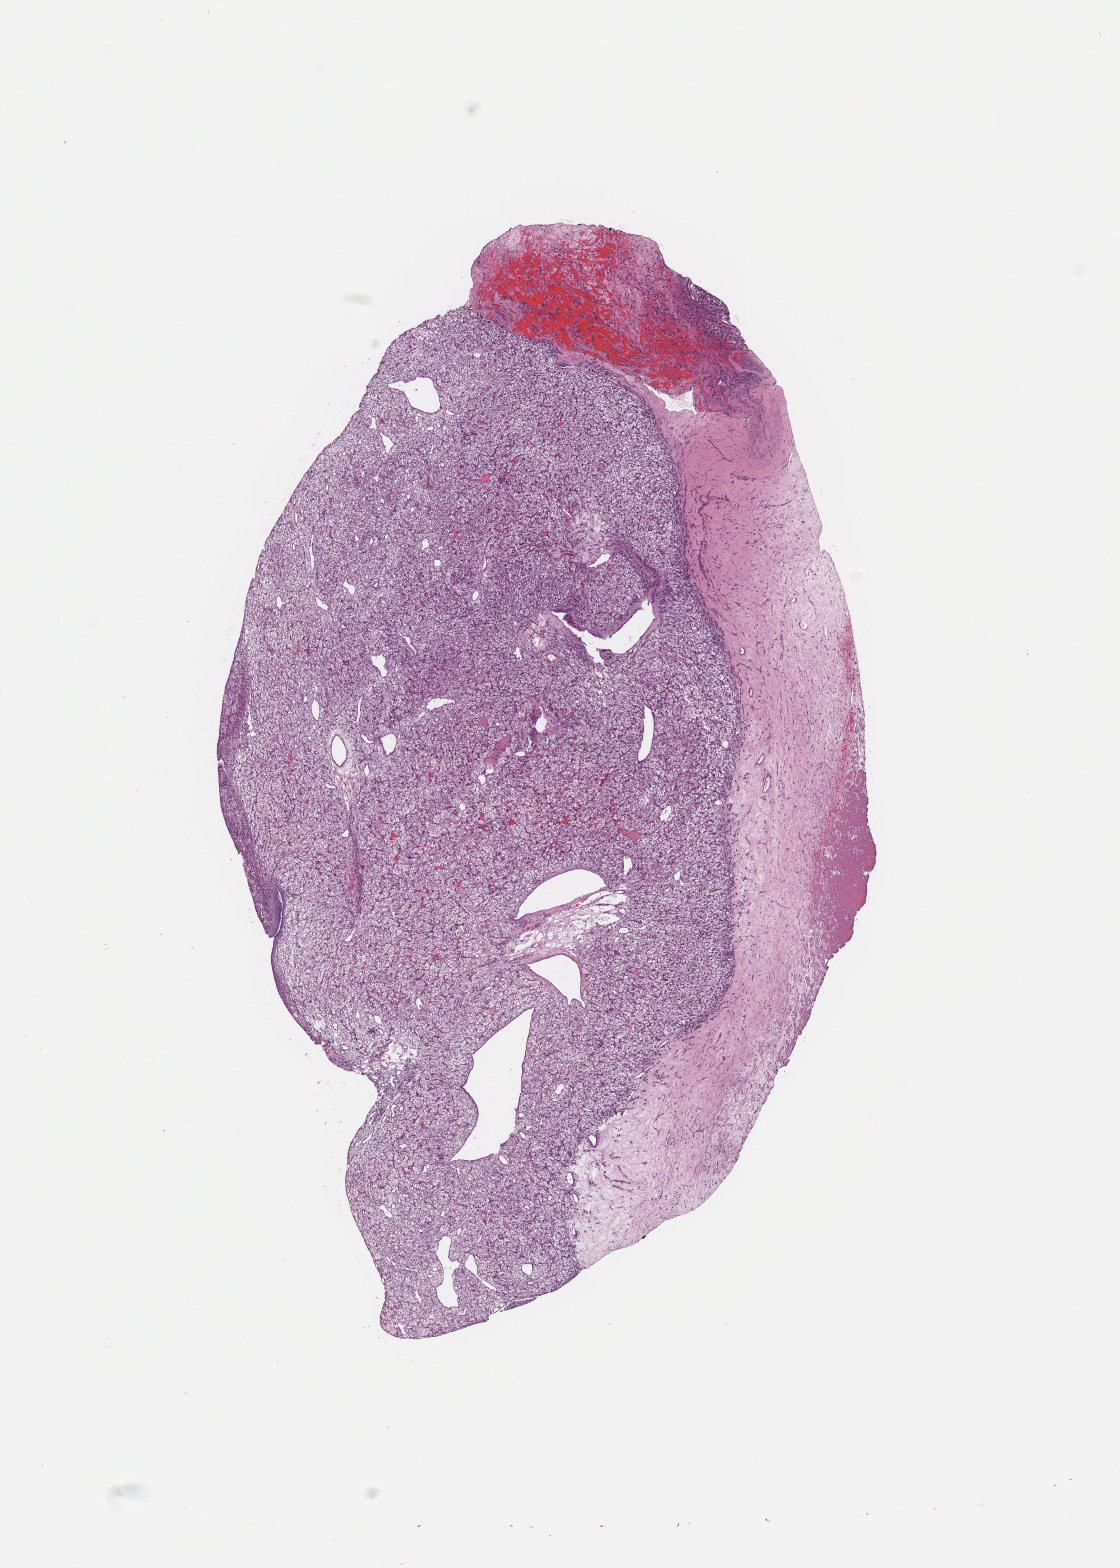
Hematoxylin and eosin (H&E) stained whole-slide image, low-resolution overview of the scanned area, about 8.9 x 12.4 mm, tumour tissue sample, sampled site: kidney. 76-year-old female patient. Histologic grade: G2 (moderately differentiated). Pathologist review of this section (percent, as recorded): tumour nuclei 90%, necrosis 0%.
Primary tumour site (as recorded): middle. AJCC pathologic stage: I. Diagnosis: Renal cell carcinoma, NOS.